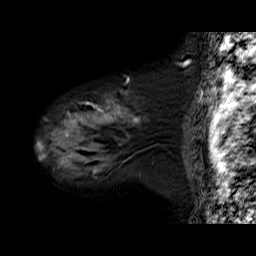
Breast MRI (dynamic contrast-enhanced), one sagittal slice. Slice 53 of 60 in the series (ordered by position). Dynamic contrast-enhanced series, time point 2 of 6 at this slice position (early post-contrast). 1.5 T. TE 6.3 ms, TR 32.9 ms. 256 × 256 image matrix, field of view 200 × 200 mm. Female patient. From the clinical record (not read from this slice): setting: breast cancer imaged before/during neoadjuvant chemotherapy; receptor status: HER2-positive.
Outlined on this slice (semi-automatic segmentation, software-assisted and operator-edited):
- analysis volume of interest (the breast-tissue region the enhancement analysis was run in; not a lesion): bounding box (x1, y1, x2, y2) in pixels: (39, 81, 149, 179)
- tumour enhancement mask (voxels above the 100 % enhancement threshold inside the analysis volume of interest): (39, 109, 139, 172)